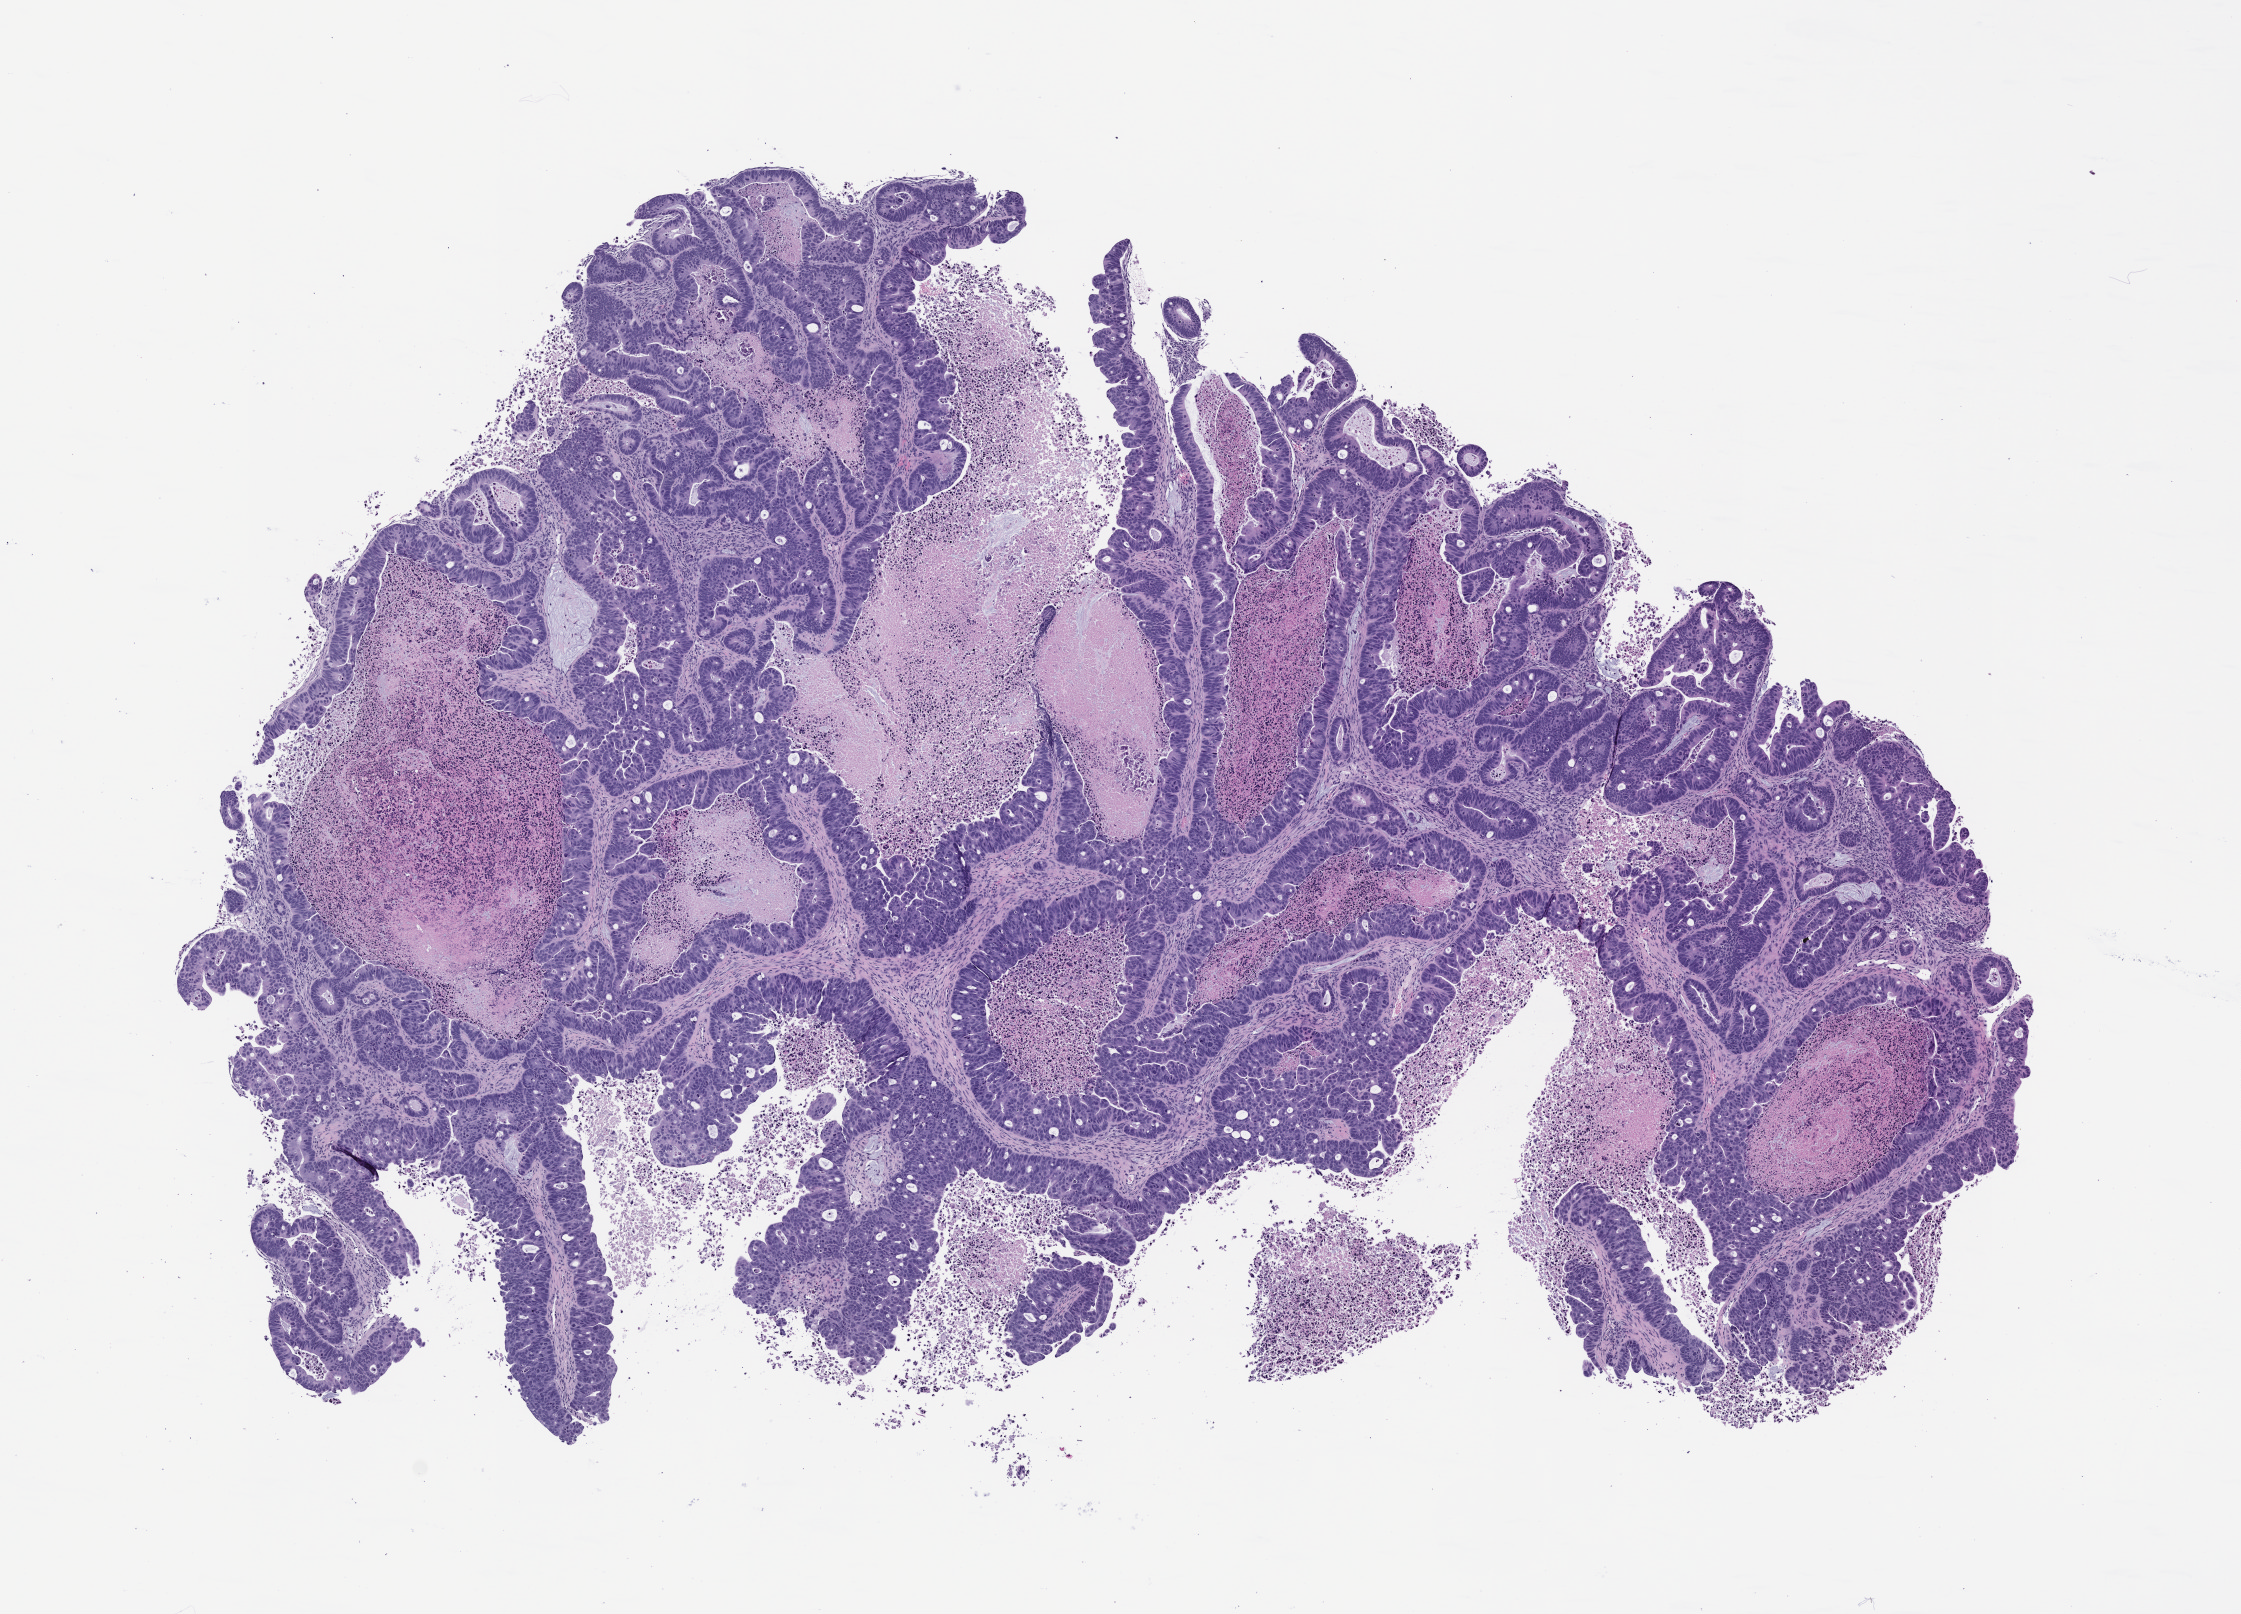
H&E whole-slide image of a patient-derived xenograft (PDX) tumor grown in a mouse, passage 0, a low-resolution overview of the entire scanned area, about 9.0 x 6.5 mm, FFPE section, tumor site category: gastrointestinal tract.
- originating patient diagnosis: Colorectal Carcinoma